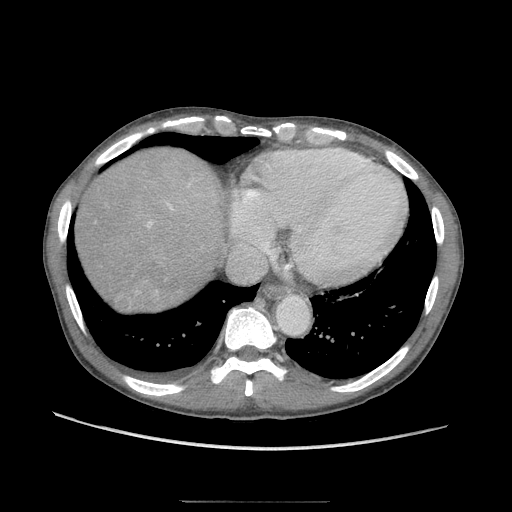
Contrast-enhanced abdominal CT (liver protocol), one axial slice. Slice 89 of 103 in the series (ordered by position). Reconstruction kernel STANDARD. Soft-tissue window (W 400 / L 40 HU). 512 × 512 image matrix. Case-level facts recorded for this patient, not image findings: diagnosis: hepatocellular carcinoma (patient treated with transarterial chemoembolisation; whether this scan precedes or follows treatment is not stated here); TNM stage (as recorded): Stage-IIIA; Child-Pugh class: A; tumour differentiation: moderately differentiated; tumour nodularity: multinodular.
Outlined on this slice (semi-automatic segmentation, software-assisted and operator-edited):
- abdominal aorta: bounding box [x1, y1, x2, y2] px = [277, 297, 308, 333]
- liver parenchyma outside the tumour (the mass and vessels are separate outlines, so this box may not span the whole liver): [78, 146, 204, 304]
- mass: [117, 293, 130, 305]